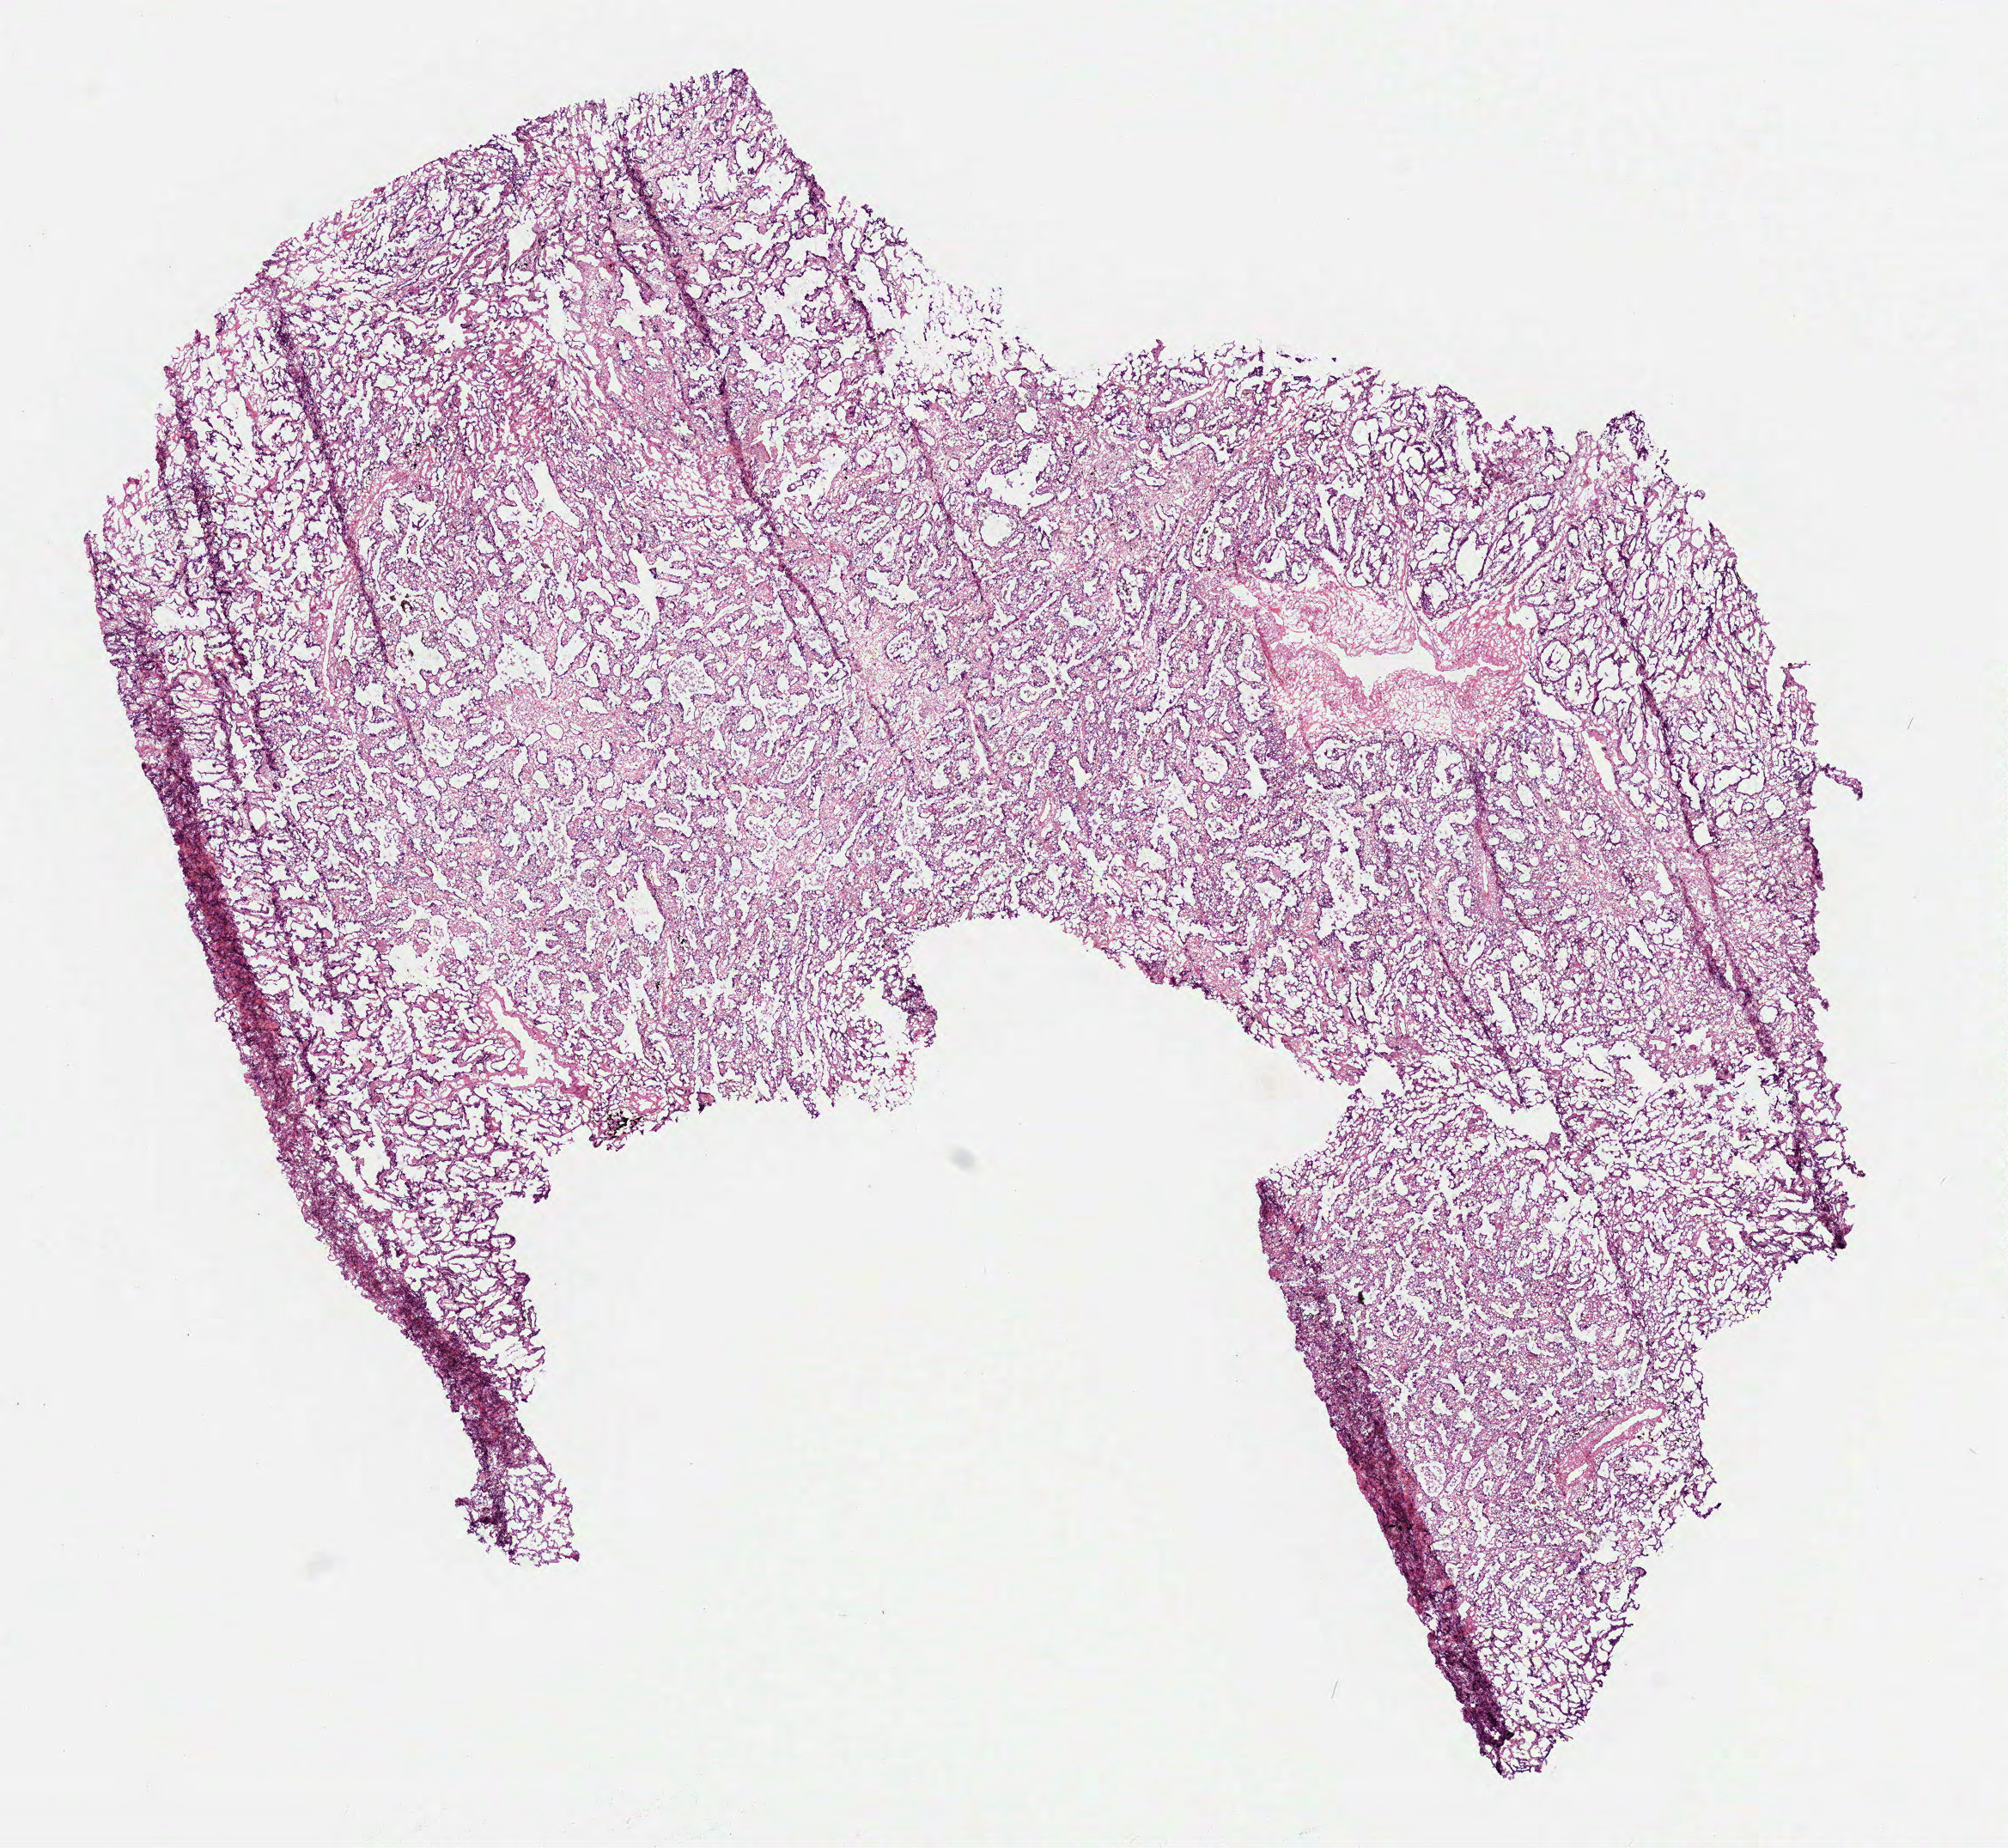
Digitized H&E-stained tissue section (whole slide) — low-resolution overview of the scanned area, about 9.4 x 8.7 mm (from a 40x scan); frozen section from the top of the tissue portion; lung, primary tumour sample. Female, age 67 years at initial diagnosis. Composition of this section per pathologist review: tumour cells 83%, tumour nuclei 75%, normal cells 0%, stromal cells 15%, necrosis 2%.
• AJCC pathologic stage: IIB (6th edition)
• diagnosis: Adenocarcinoma, NOS (upper lobe, lung)